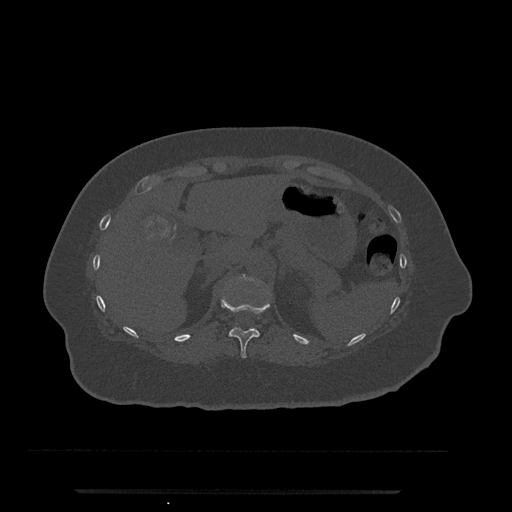
CT including the spine, one axial slice. Position 211 of 797 along the scan axis. Bone window (W 1800 / L 400 HU). 0.5 mm slice thickness. 512 × 512 image matrix. Female patient, age 51 years. Case-level facts recorded for this patient, not image findings: primary cancer: neuro; vertebrae with lytic lesions (as recorded): T8.
Structures marked on this image (semi-automatically segmented with operator editing):
- T11 vertebra: box from (x=221, y=295) to (x=270, y=358) px